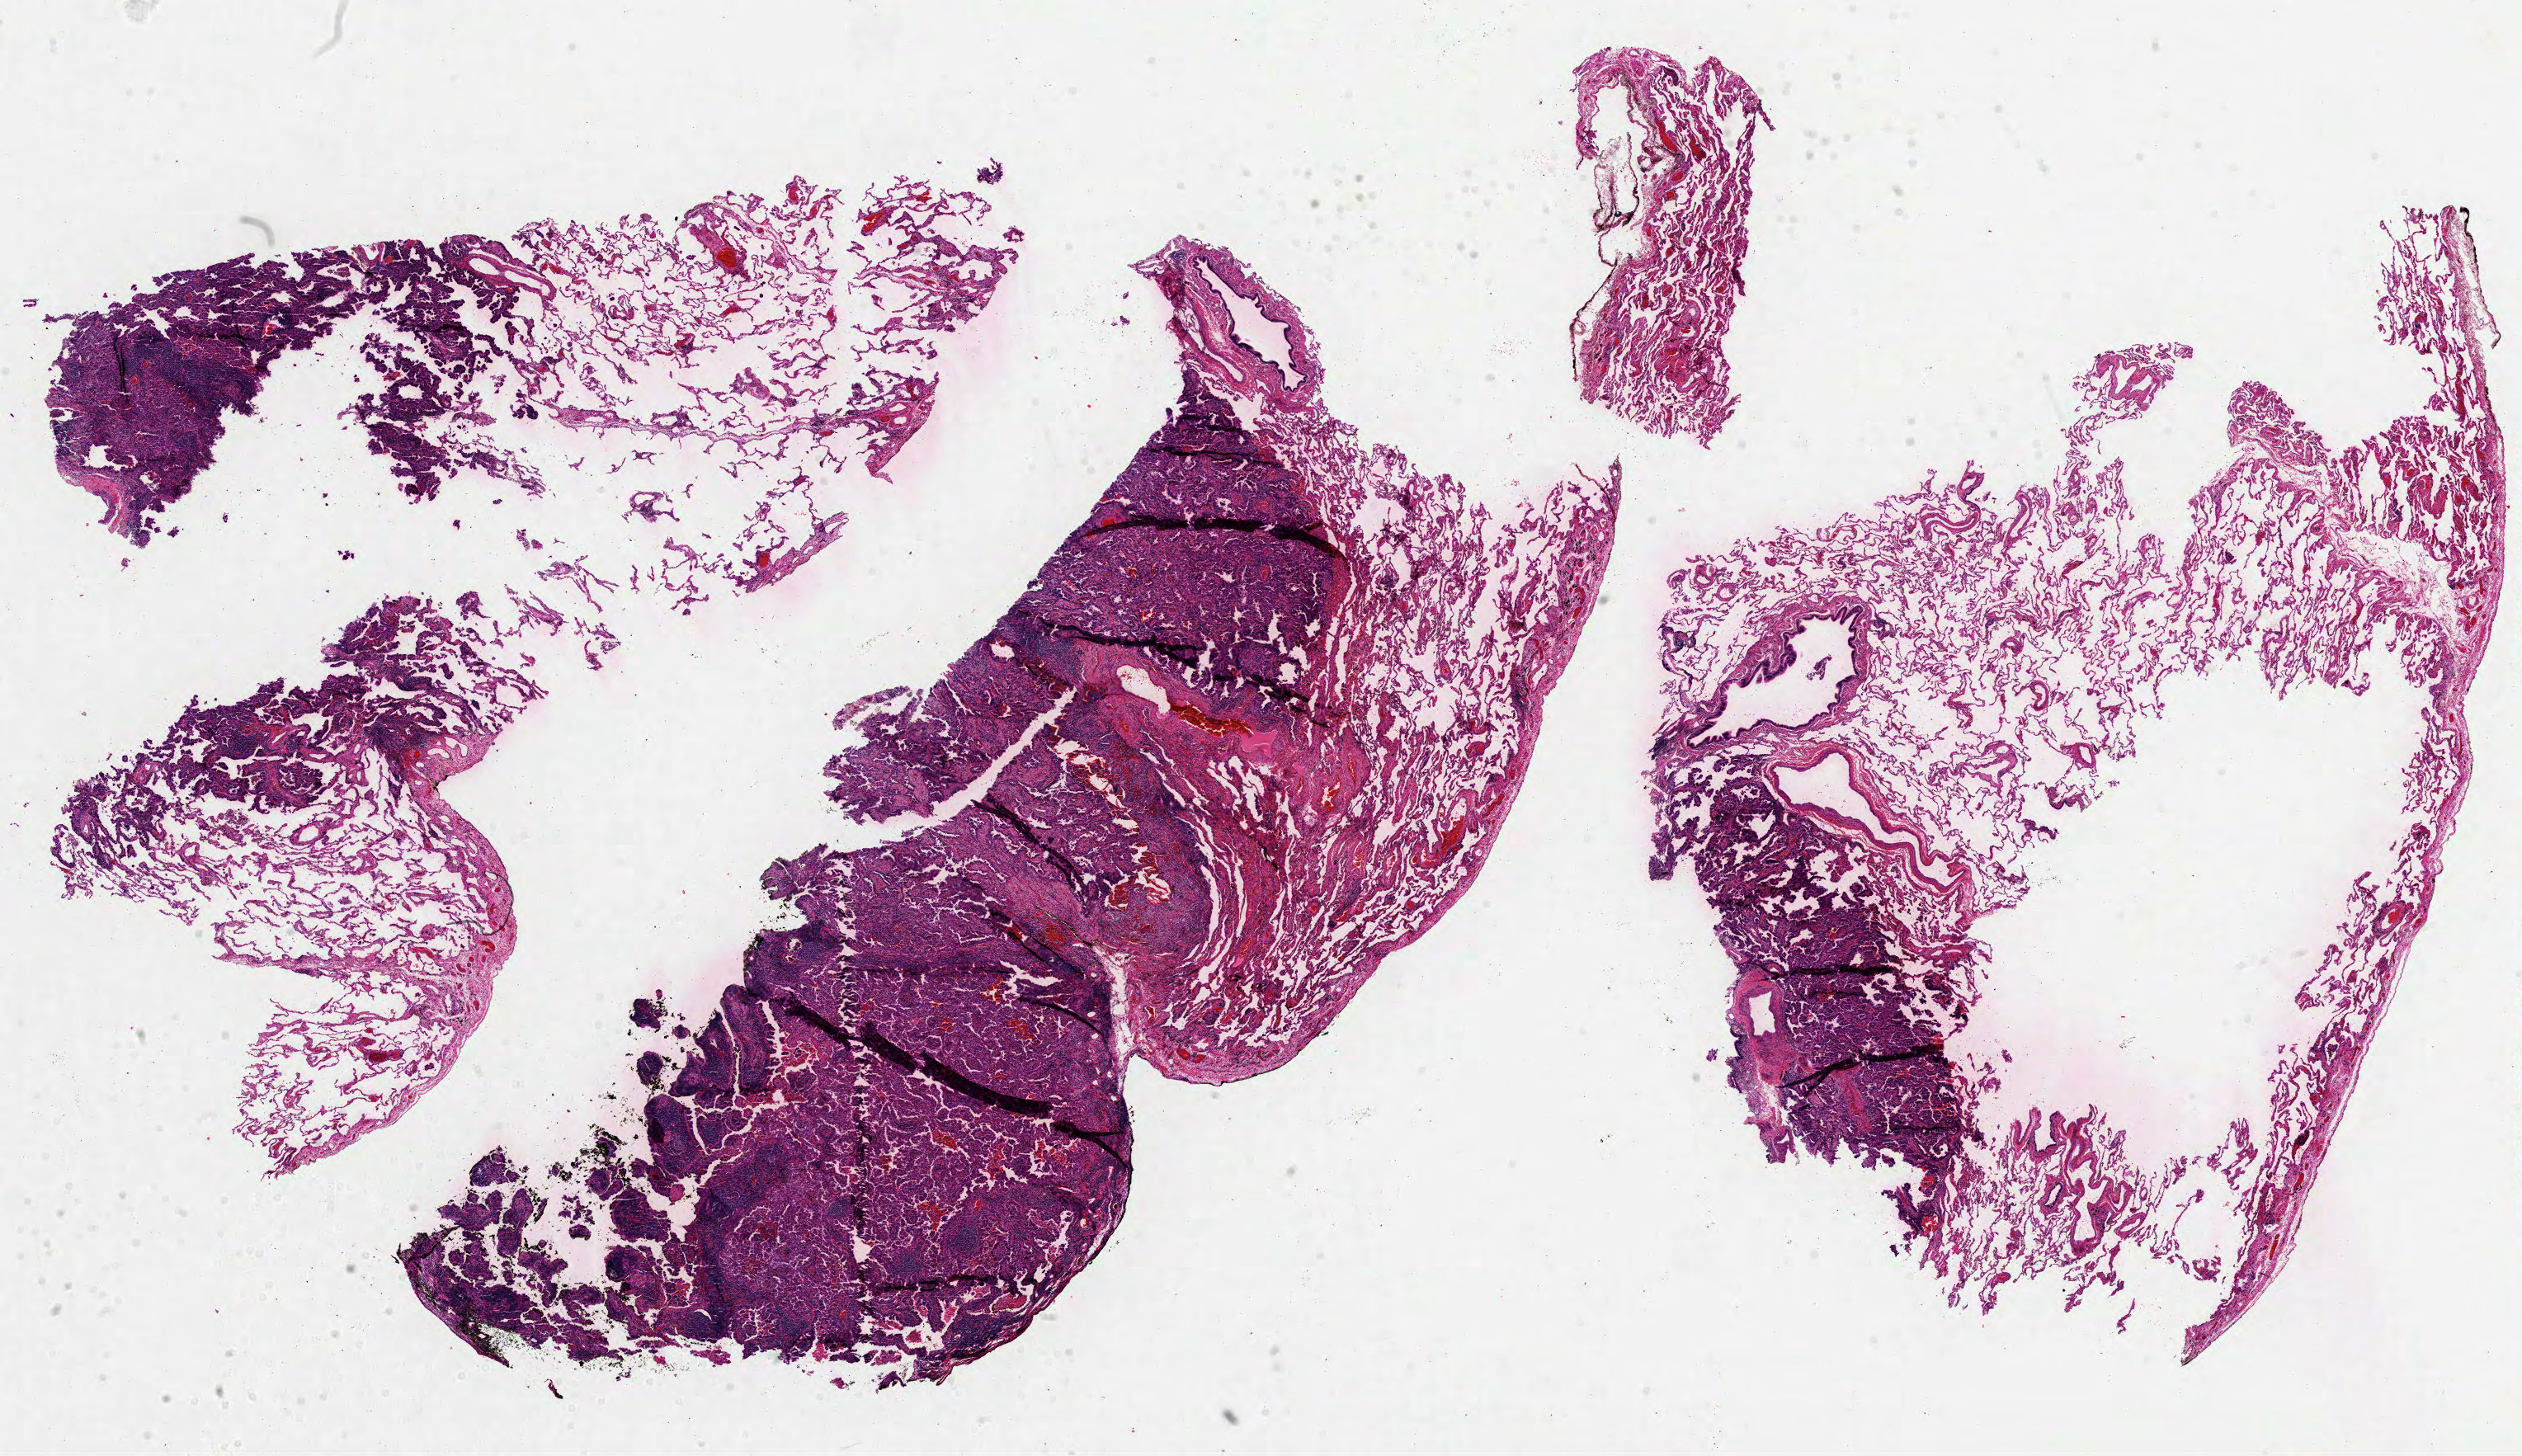
H&E-stained whole-slide image, whole scanned area (about 24.7 x 14.2 mm) shown as a low-resolution overview; FFPE section; primary tumour sample from the lung. Patient: female, age at initial diagnosis 74 years.
AJCC pathologic stage: IA (3rd edition). Diagnosis: Adenocarcinoma, NOS.